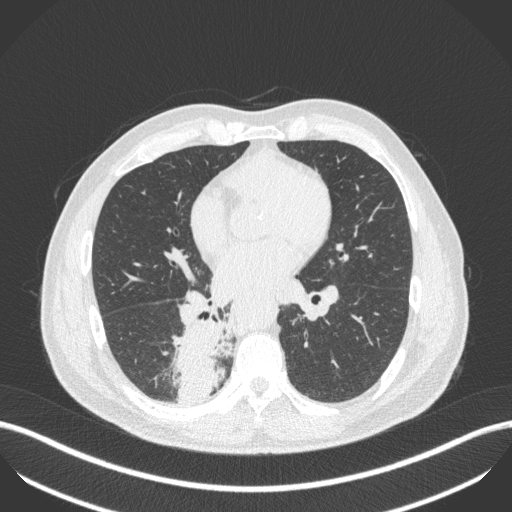
Chest CT, one axial slice. Slice 223 of 451 in the series (ordered by position). 100 kVp. Lung window (W 1500 / L -600 HU). 1 mm slice thickness. 512 × 512 image matrix, field of view 400 × 400 mm. Patient: male, 61 years. Case-level facts recorded for this patient, not image findings: clinical TNM (as recorded): T1 N0 M0; histopathological grade: G3.
Annotated regions visible in this slice (rectangle marked by the reading radiologist):
- lung tumour (recorded histology: small cell carcinoma): bounding box (x1, y1, x2, y2) in pixels: (178, 321, 229, 406)